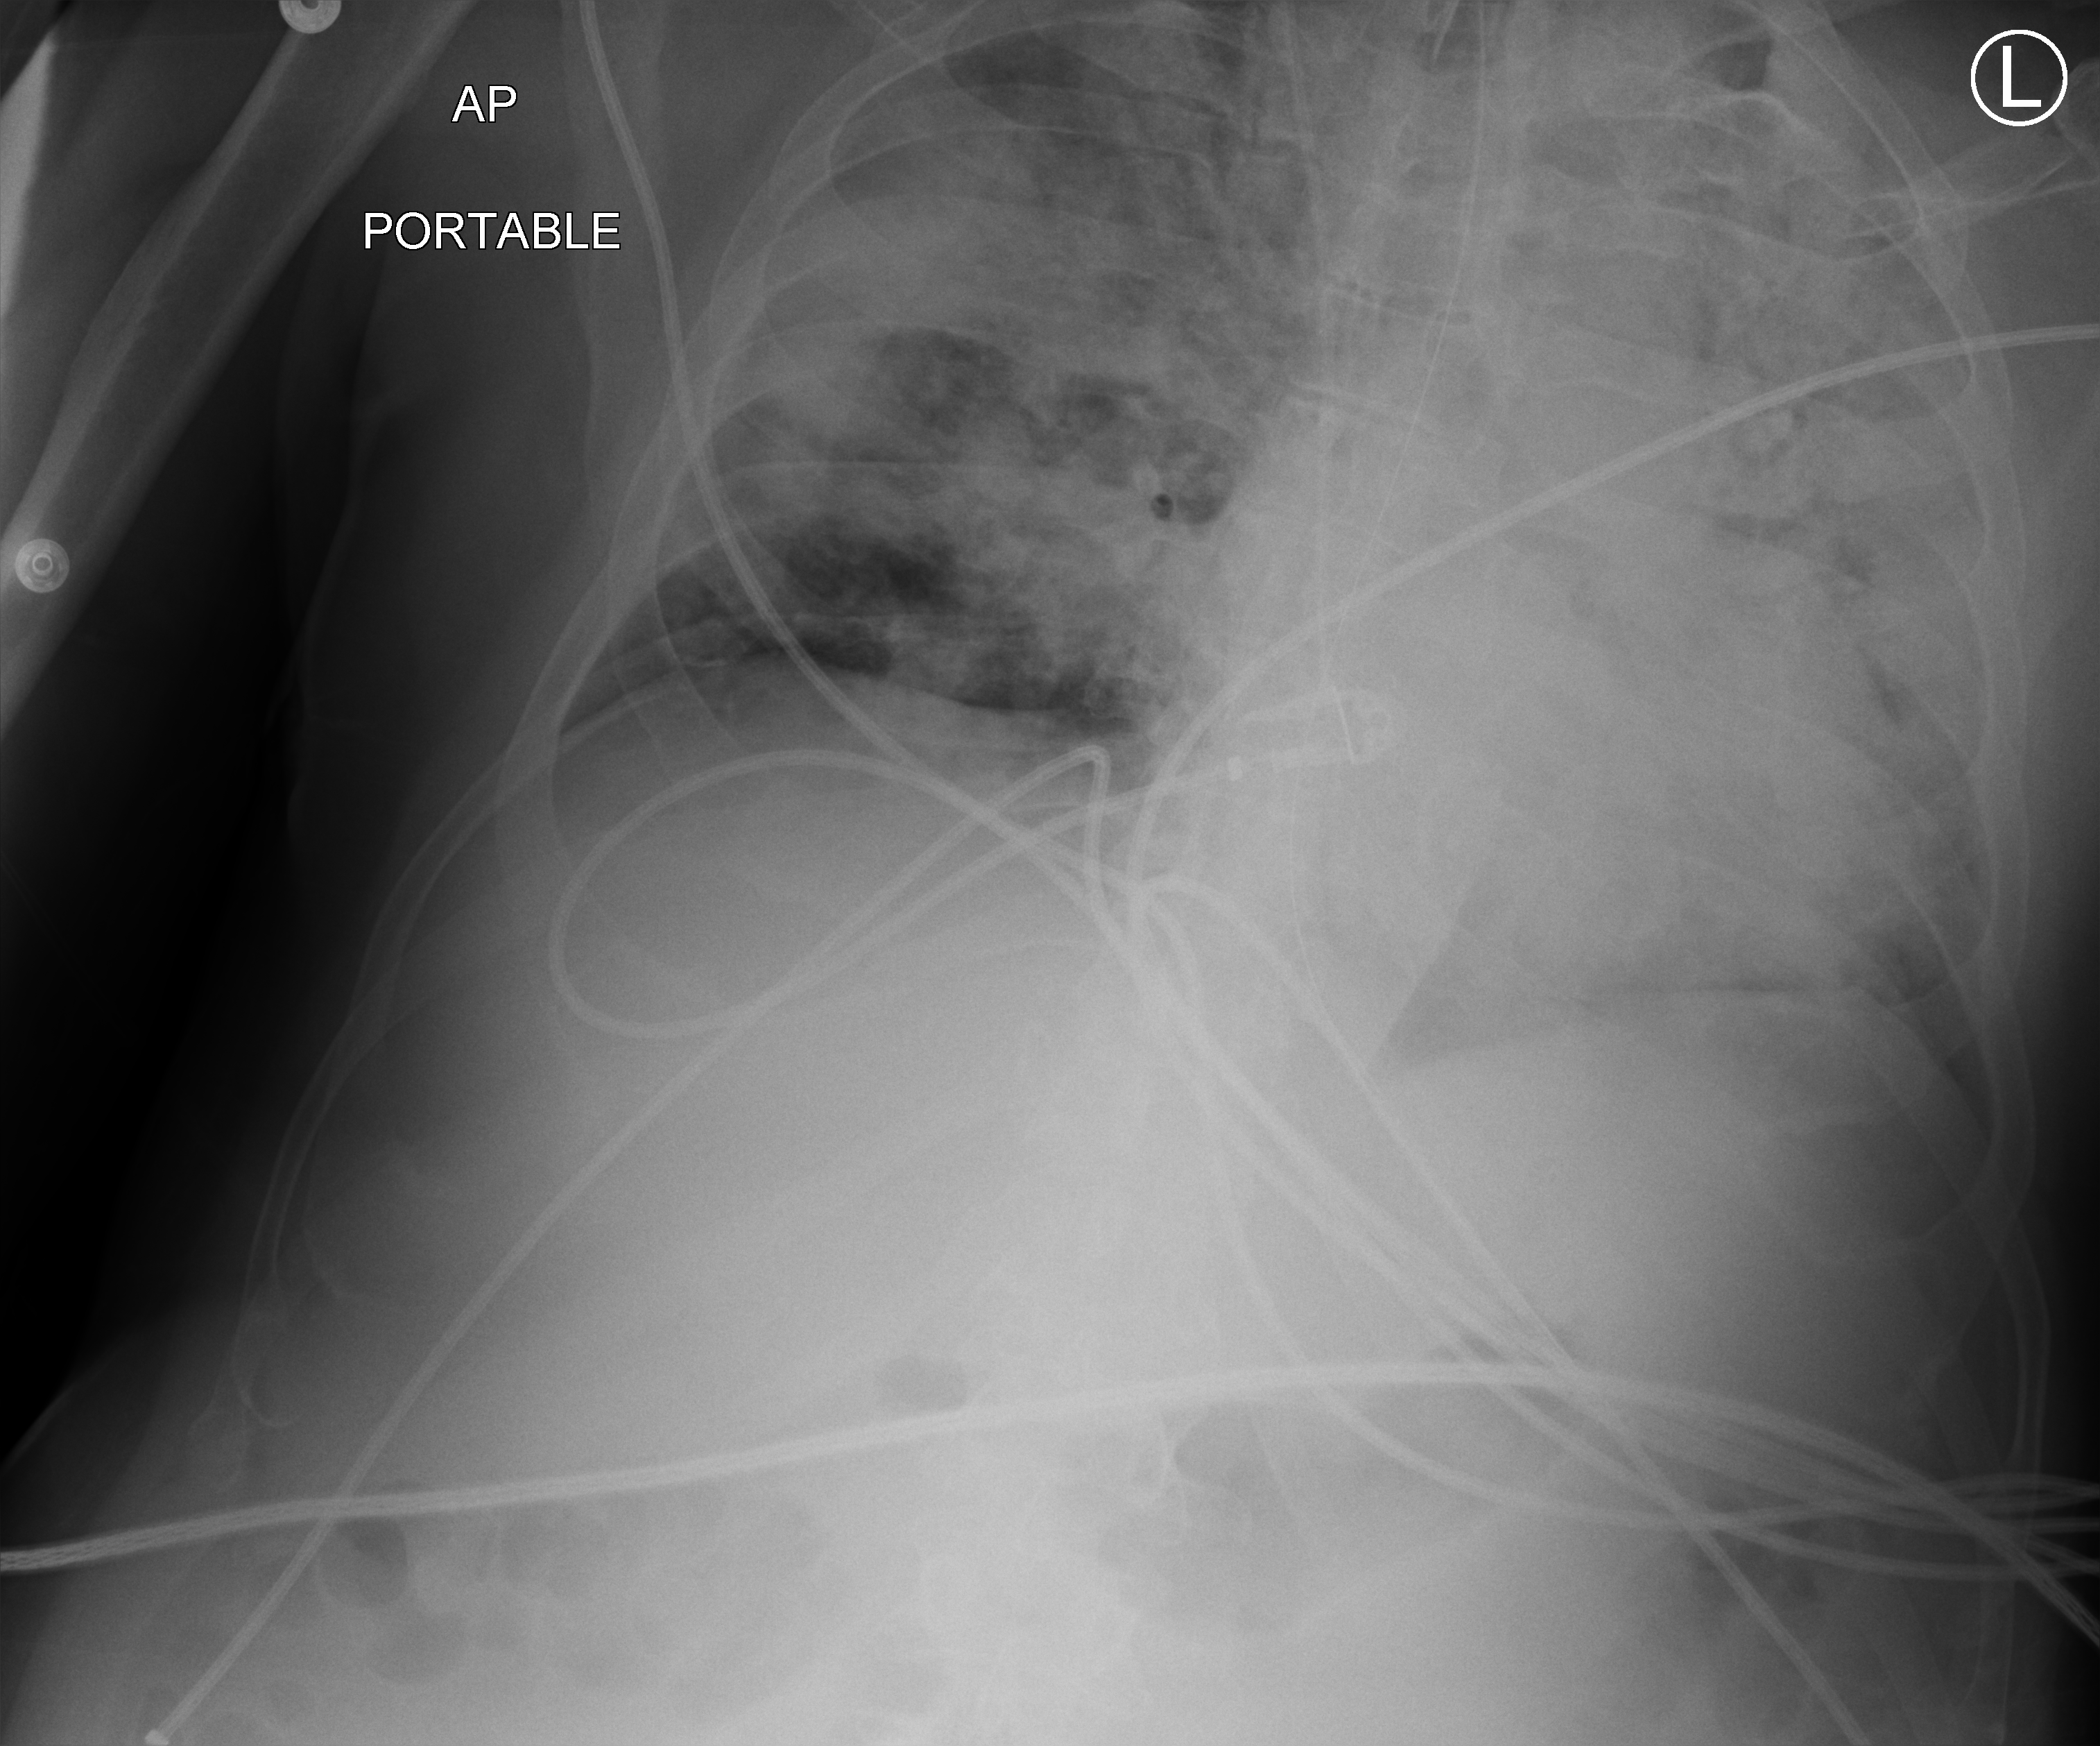
Chest X-ray (portable). Male patient hospitalised with COVID-19, age 18–59 years.
From the hospital-stay record, not from the radiograph (when in the stay this image was taken is not recorded): mechanically ventilated during this hospital stay: yes; admitted to intensive care during this hospital stay: yes.